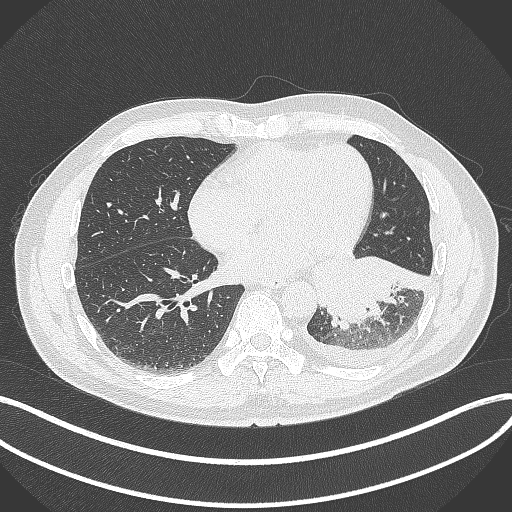
Chest CT, one axial slice; position 137 of 342 along the scan axis; reconstruction kernel B70f; lung window (W 1500 / L -600 HU); 1 mm slice thickness; 512 × 512 image matrix, field of view 400 × 400 mm. Male patient, age 58 years. Case-level facts recorded for this patient, not image findings: clinical TNM (as recorded): T3 N1 M1b; histopathological grade: G3.
Outlined on this slice (bounding box drawn by a radiologist):
- lung tumour (recorded histology: small cell carcinoma): bounding box (x1, y1, x2, y2) in pixels: (308, 244, 439, 328)